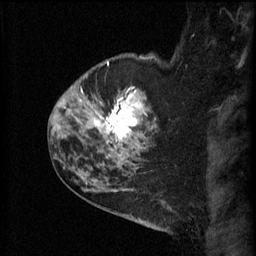
Breast MRI (dynamic contrast-enhanced), one sagittal slice. Slice 46 of 60 in the series (ordered by position). 3 images stored at this slice position (order not interpretable as contrast timing). 1.5 T. TE 4.2 ms, TR 11 ms. 2.3 mm slice thickness. 256 × 256 image matrix, field of view 180 × 180 mm. Female patient, age 52 years.
Annotated regions visible in this slice (semi-automatic segmentation, software-assisted and operator-edited):
- analysis volume of interest (the breast-tissue region the enhancement analysis was run in; not a lesion): box from (x=86, y=76) to (x=159, y=157) px
- tumour enhancement mask (voxels above the 70 % enhancement threshold inside the analysis volume of interest): (x=94, y=90)–(x=146, y=149)